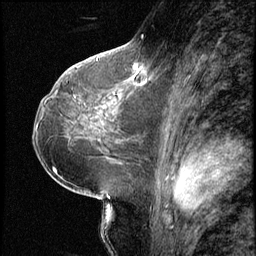
Breast MRI (dynamic contrast-enhanced), one sagittal slice; slice 35 of 66 in the series (ordered by position); 3 images stored at this slice position (order not interpretable as contrast timing); 1.5 T; TE 4.2 ms, TR 8.7 ms; 2.5 mm slice thickness; 256 × 256 image matrix, field of view 180 × 180 mm. Female patient, age 38 years. Case-level facts recorded for this patient, not image findings: setting: breast cancer imaged before/during neoadjuvant chemotherapy; receptor status: triple-negative.
Structures marked on this image (semi-automatically segmented with operator editing):
- analysis volume of interest (the breast-tissue region the enhancement analysis was run in; not a lesion): box from (x=128, y=57) to (x=149, y=78) px
- tumour enhancement mask (voxels above the 140 % enhancement threshold inside the analysis volume of interest): (x=133, y=64)–(x=142, y=71)